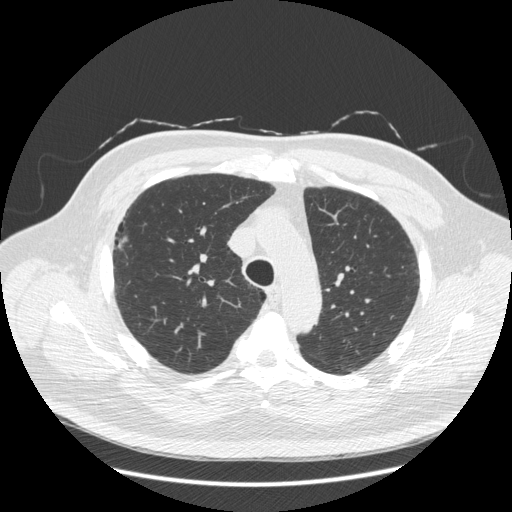
Axial slice from a low-dose chest CT screening exam, second annual screen, lung window (W 1500 / L -600 HU), 1.25 mm slice thickness, 120 kVp, slice 70 of 281 in the series, 512 × 512 image matrix, field of view 400 × 400 mm. Male, age 66 years at enrolment. Current smoker at enrolment.
Lesion marked by an expert reader, bounding box <102,213,142,266> (left, top, right, bottom; pixels). The screening reader recorded 2 non-calcified nodules or masses ≥4 mm on this exam; which of them this box marks is not recorded. Official screen result: positive, other. Later outcome: lung cancer diagnosed 403 days after this screen — non-small cell carcinoma, right upper lobe, stage IV (AJCC 6th edition), 50 mm at pathology.